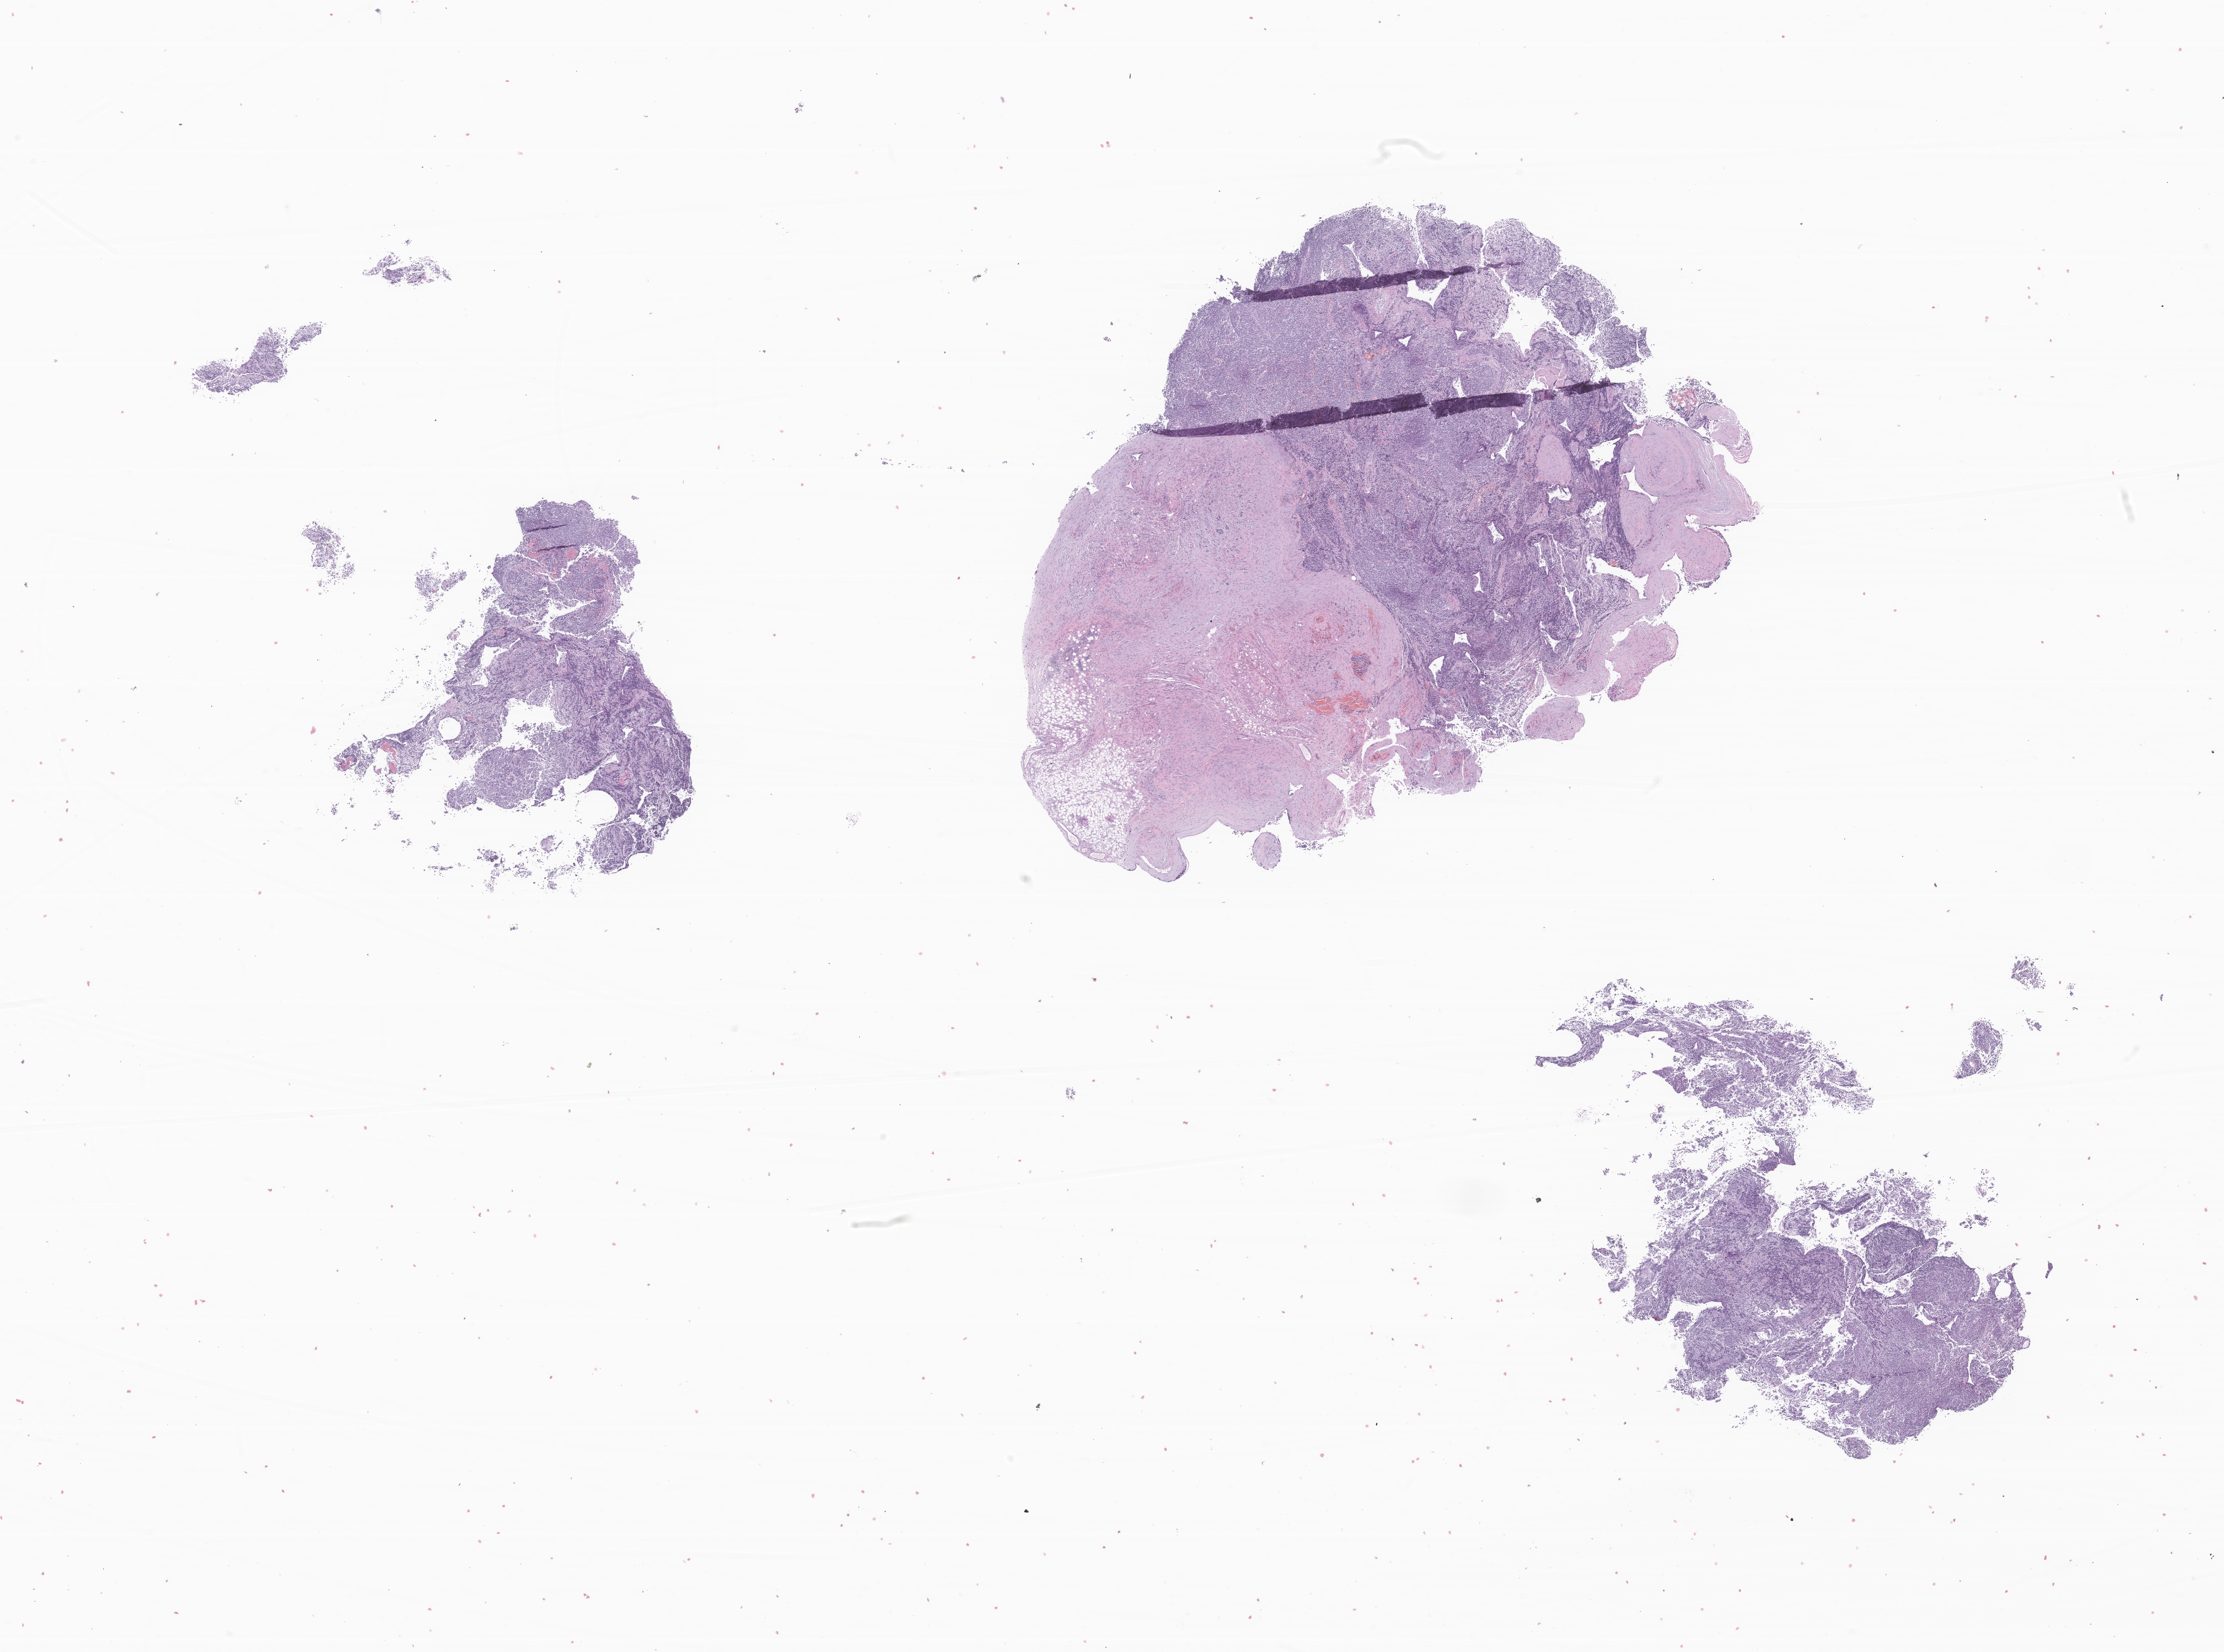
Whole-slide image, H&E stain of tumor tissue from the adrenal gland, a low-resolution overview of the entire scanned area, about 22.3 x 16.6 mm, formalin-fixed, paraffin-embedded (FFPE) tissue. Male patient, age 957 days (about 2.6 years).
Recorded diagnosis: Neuroblastoma, NOS.